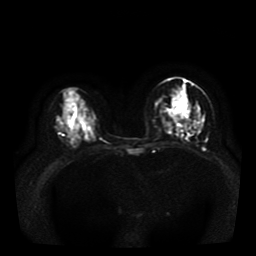
Breast MRI, one axial slice; diffusion-weighted series; image 2 of 4 stored at this slice position (different b-values; order by instance number); 1.5 T; 5 mm slice thickness; 256 × 256 image matrix, field of view 330 × 330 mm. Female patient.
Annotated regions visible in this slice (expert manual segmentation):
- tumour on diffusion-weighted imaging: bounding box <175,117,177,120> (left, top, right, bottom; pixels)